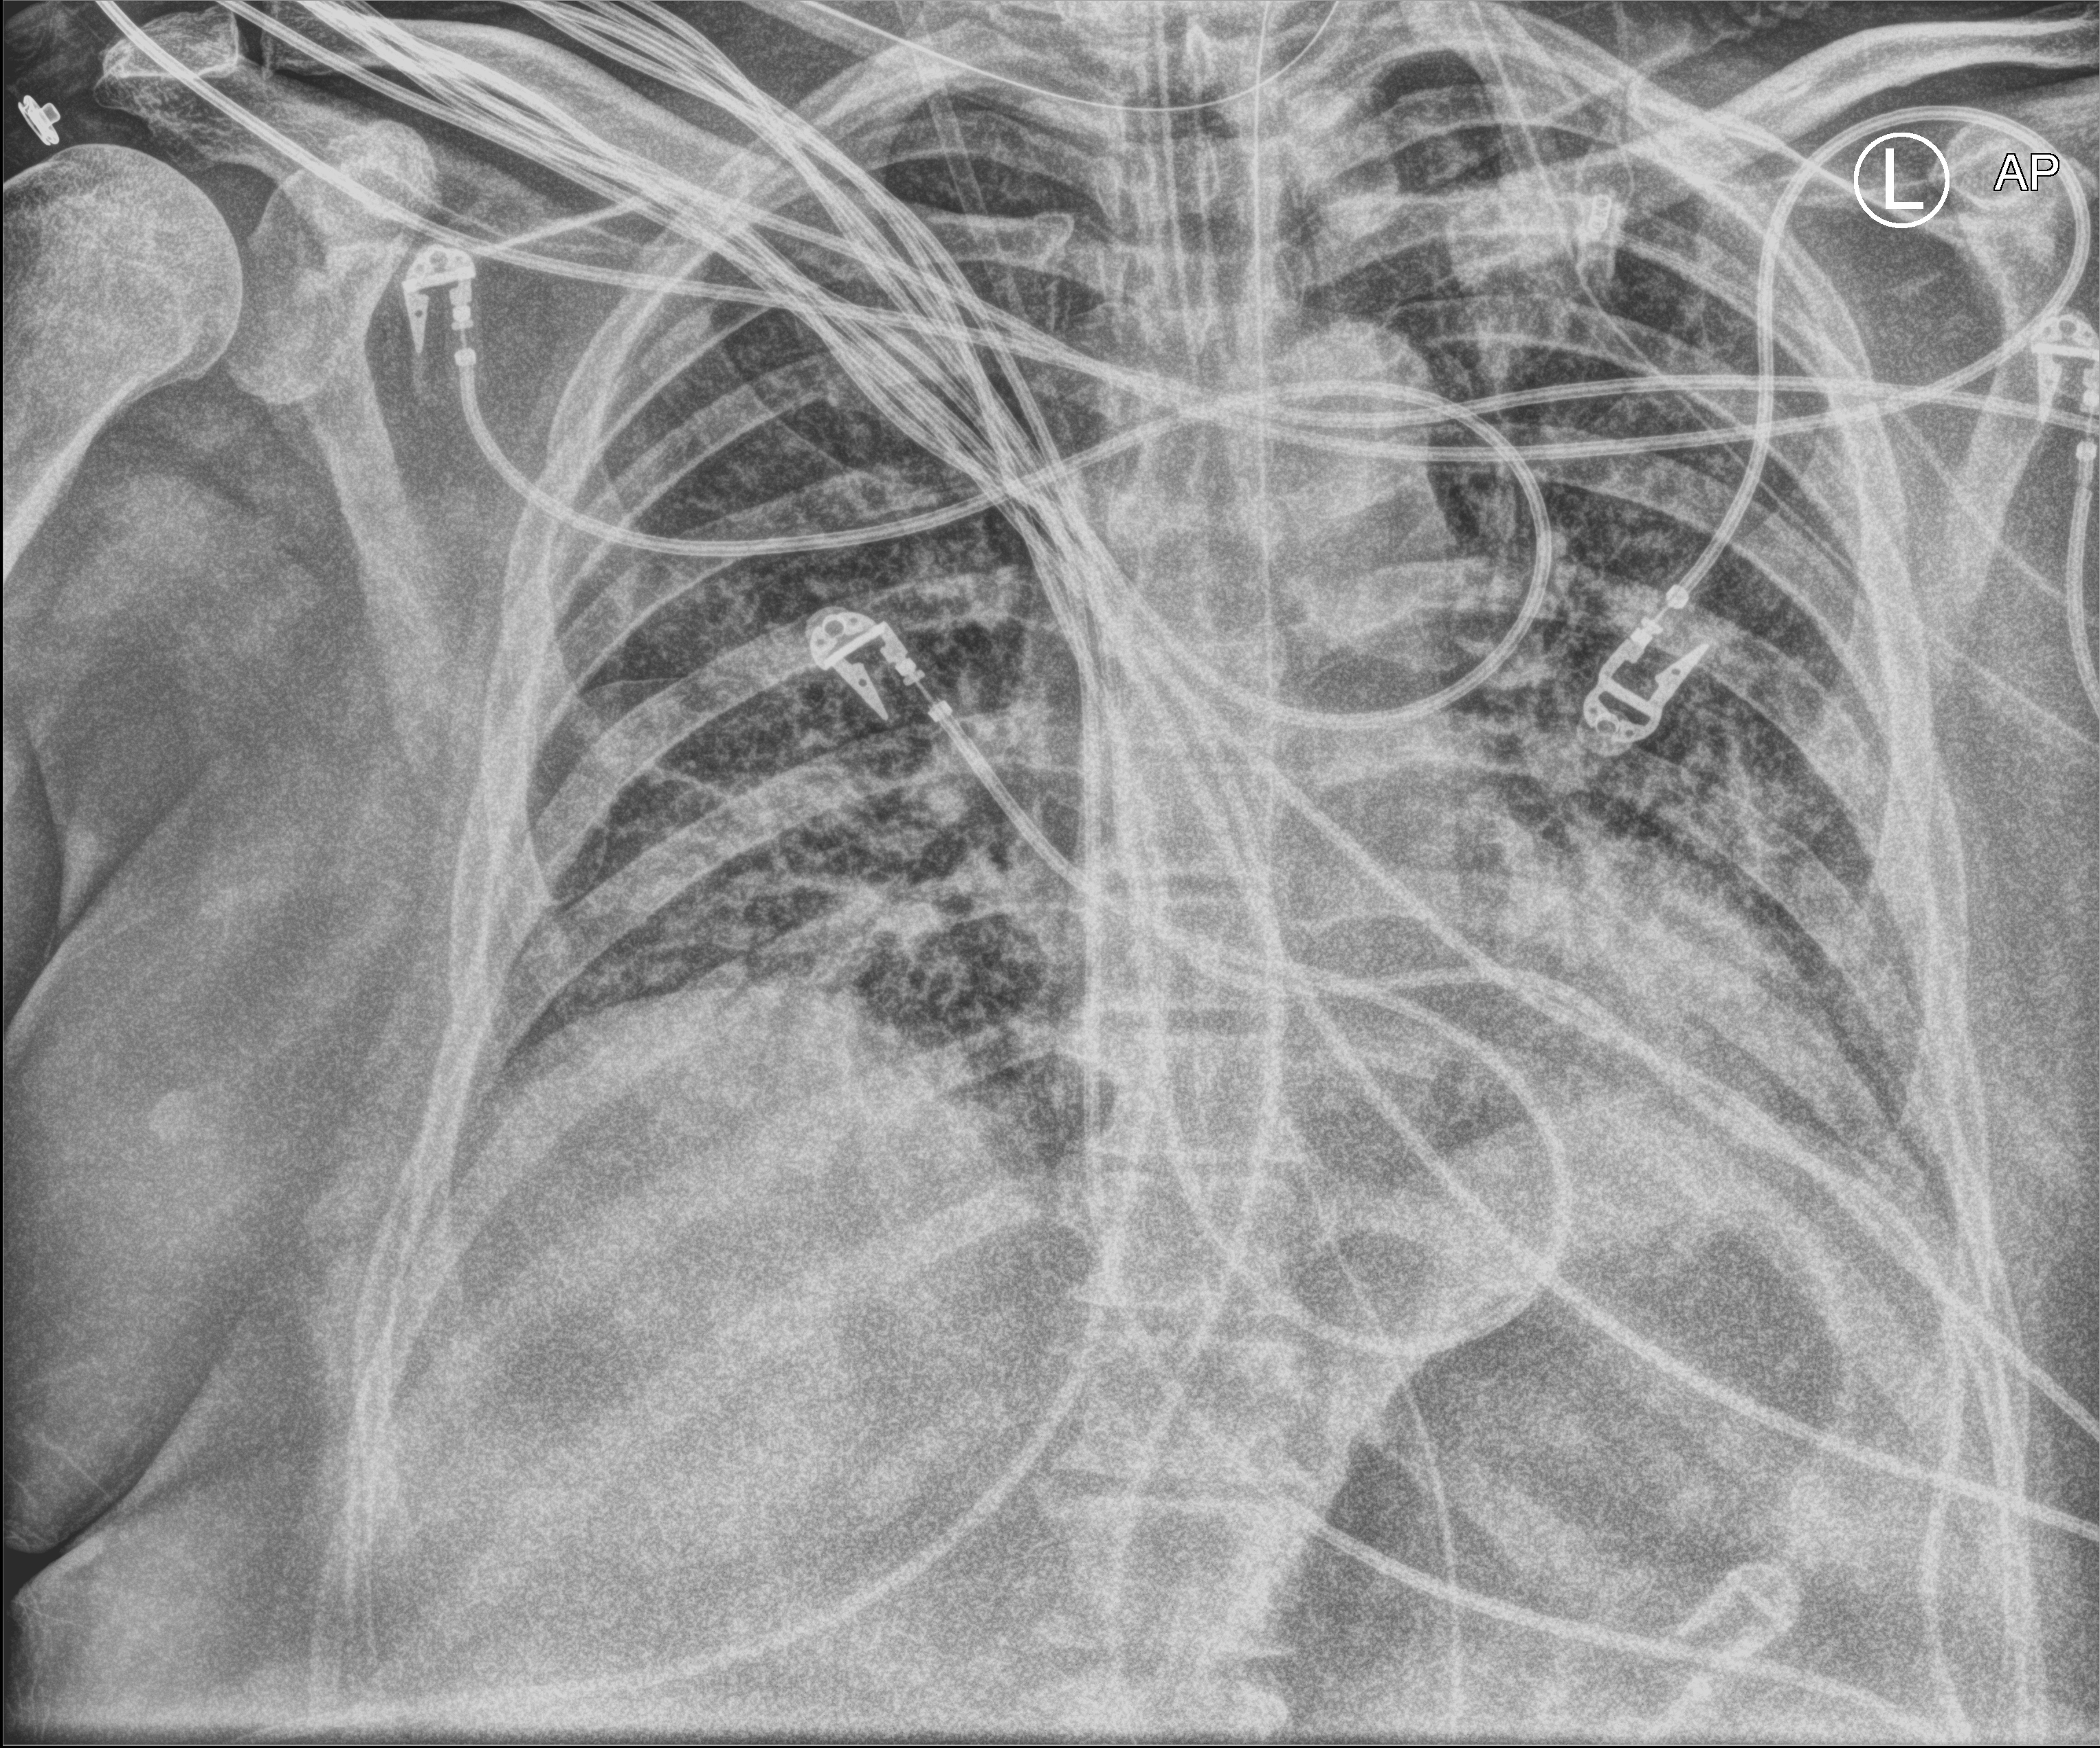
Bedside chest radiograph (computed radiography). Male patient hospitalised with COVID-19, age 60–74 years.
From the hospital-stay record, not from the radiograph (when in the stay this image was taken is not recorded): hypertension (admission record): yes; mechanically ventilated during this hospital stay: yes.